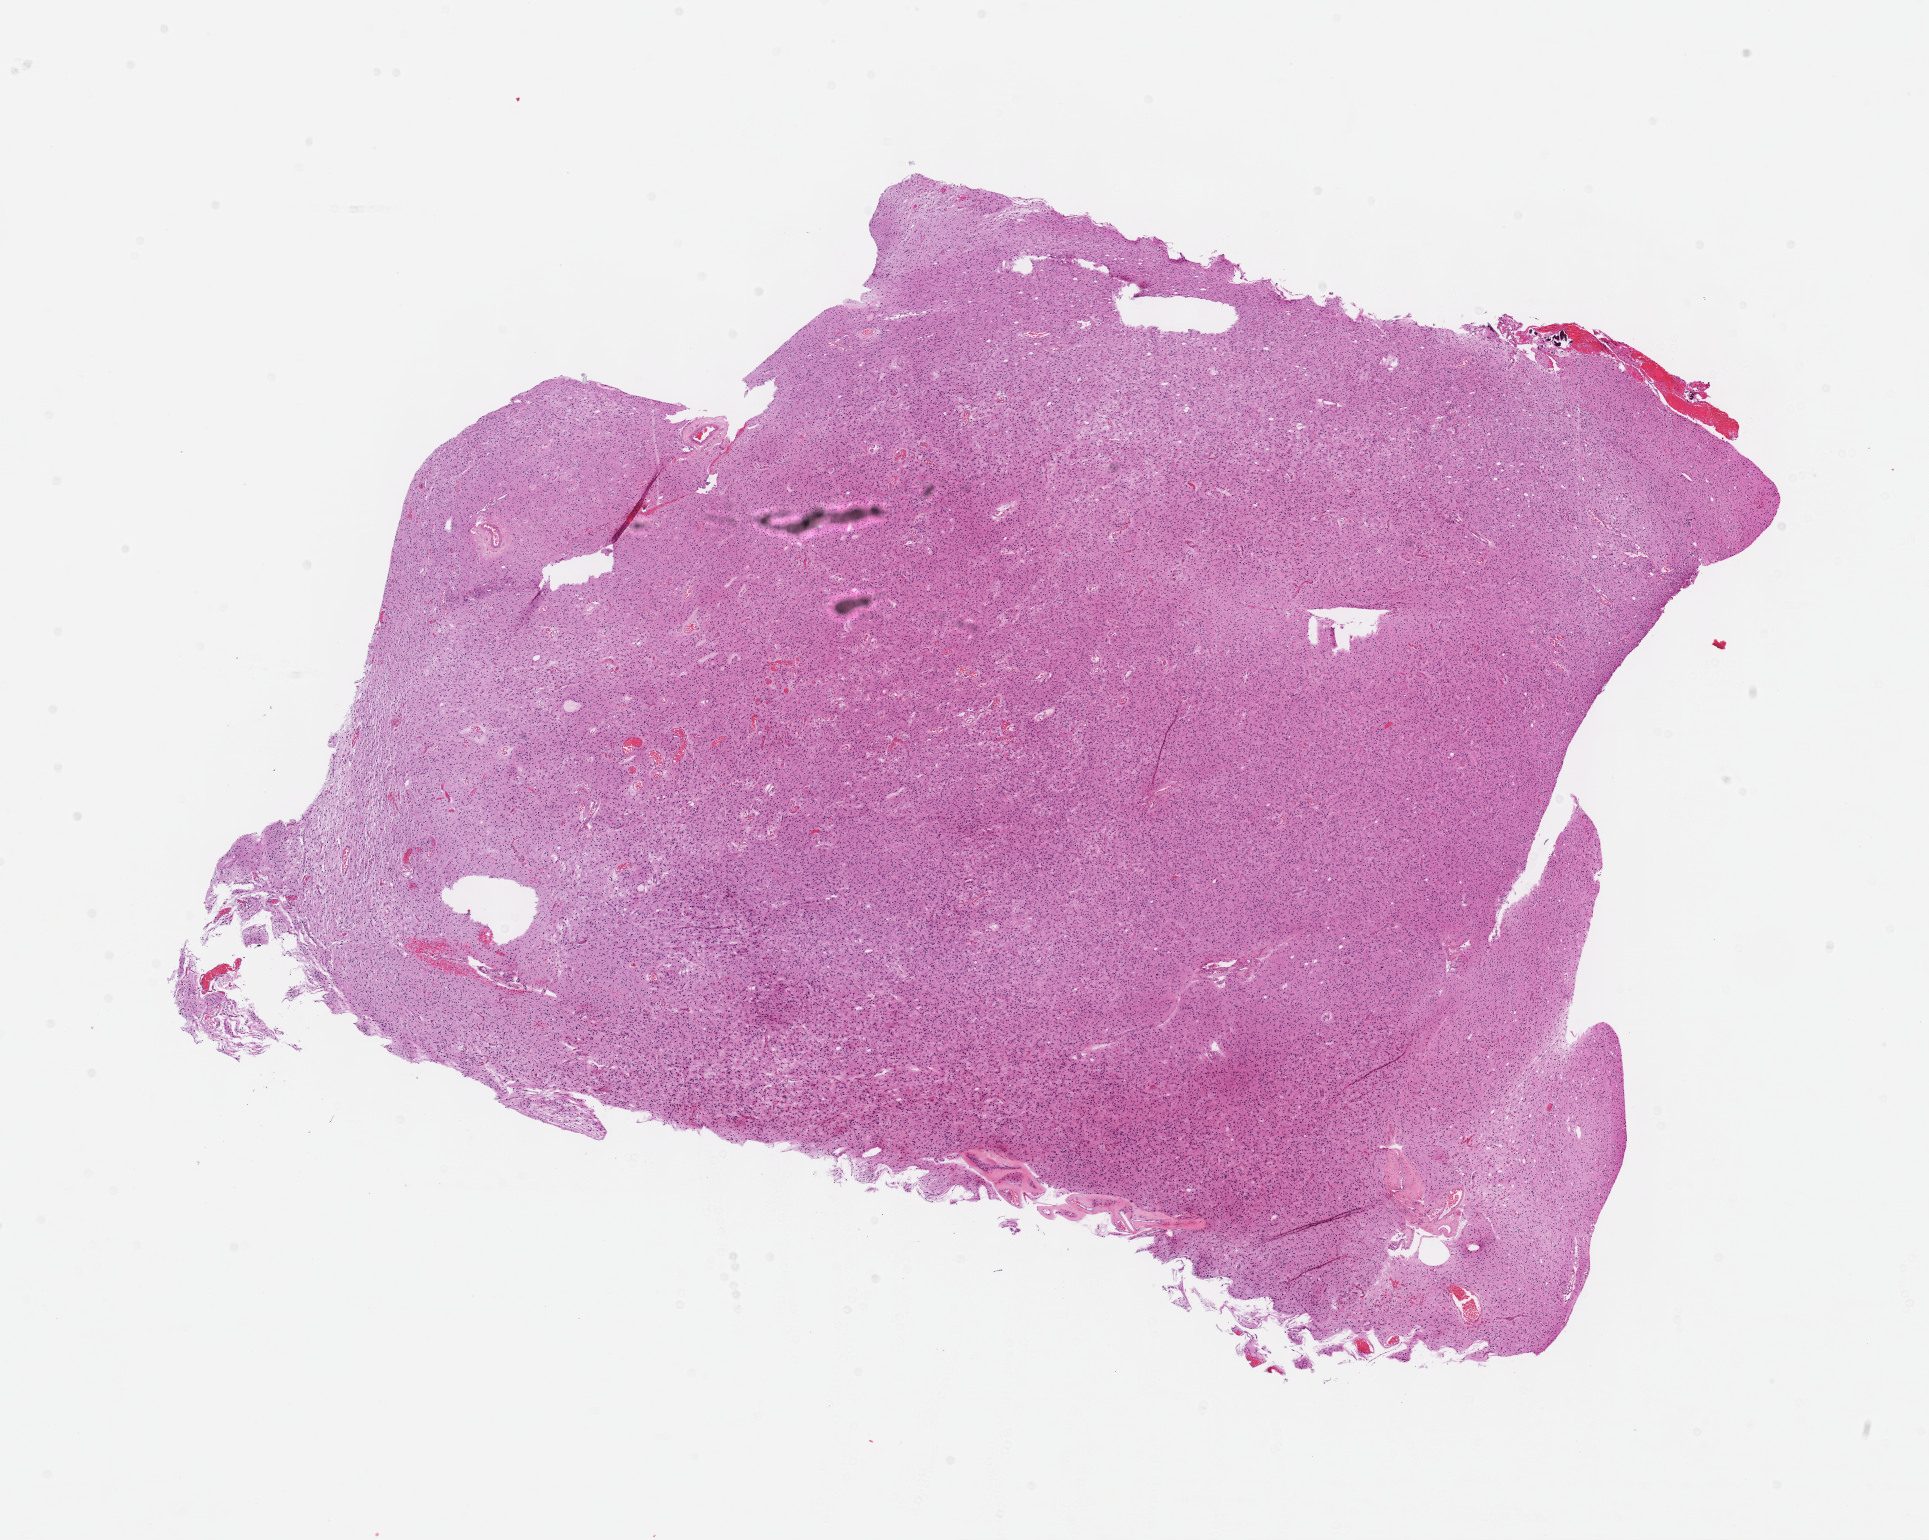
Digitized Hematoxylin and eosin (H&E) stained tissue section (whole slide) — shown as a low-resolution overview of the whole scanned area (about 15.6 x 12.5 mm). Frozen section from the top of the tissue portion. Brain, primary tumour sample. Patient: male, age at initial diagnosis 65 years. Histologic grade: G2 (moderately differentiated). Composition of this section per pathologist review: tumour cells 50%, tumour nuclei 90%, normal cells 10%, stromal cells 40%, necrosis 0%. Inflammatory infiltration, as recorded: lymphocyte infiltration 0%, monocyte infiltration 0%, neutrophil infiltration 0%.
• histologic diagnosis: Astrocytoma, NOS (cerebrum)
• laterality: right